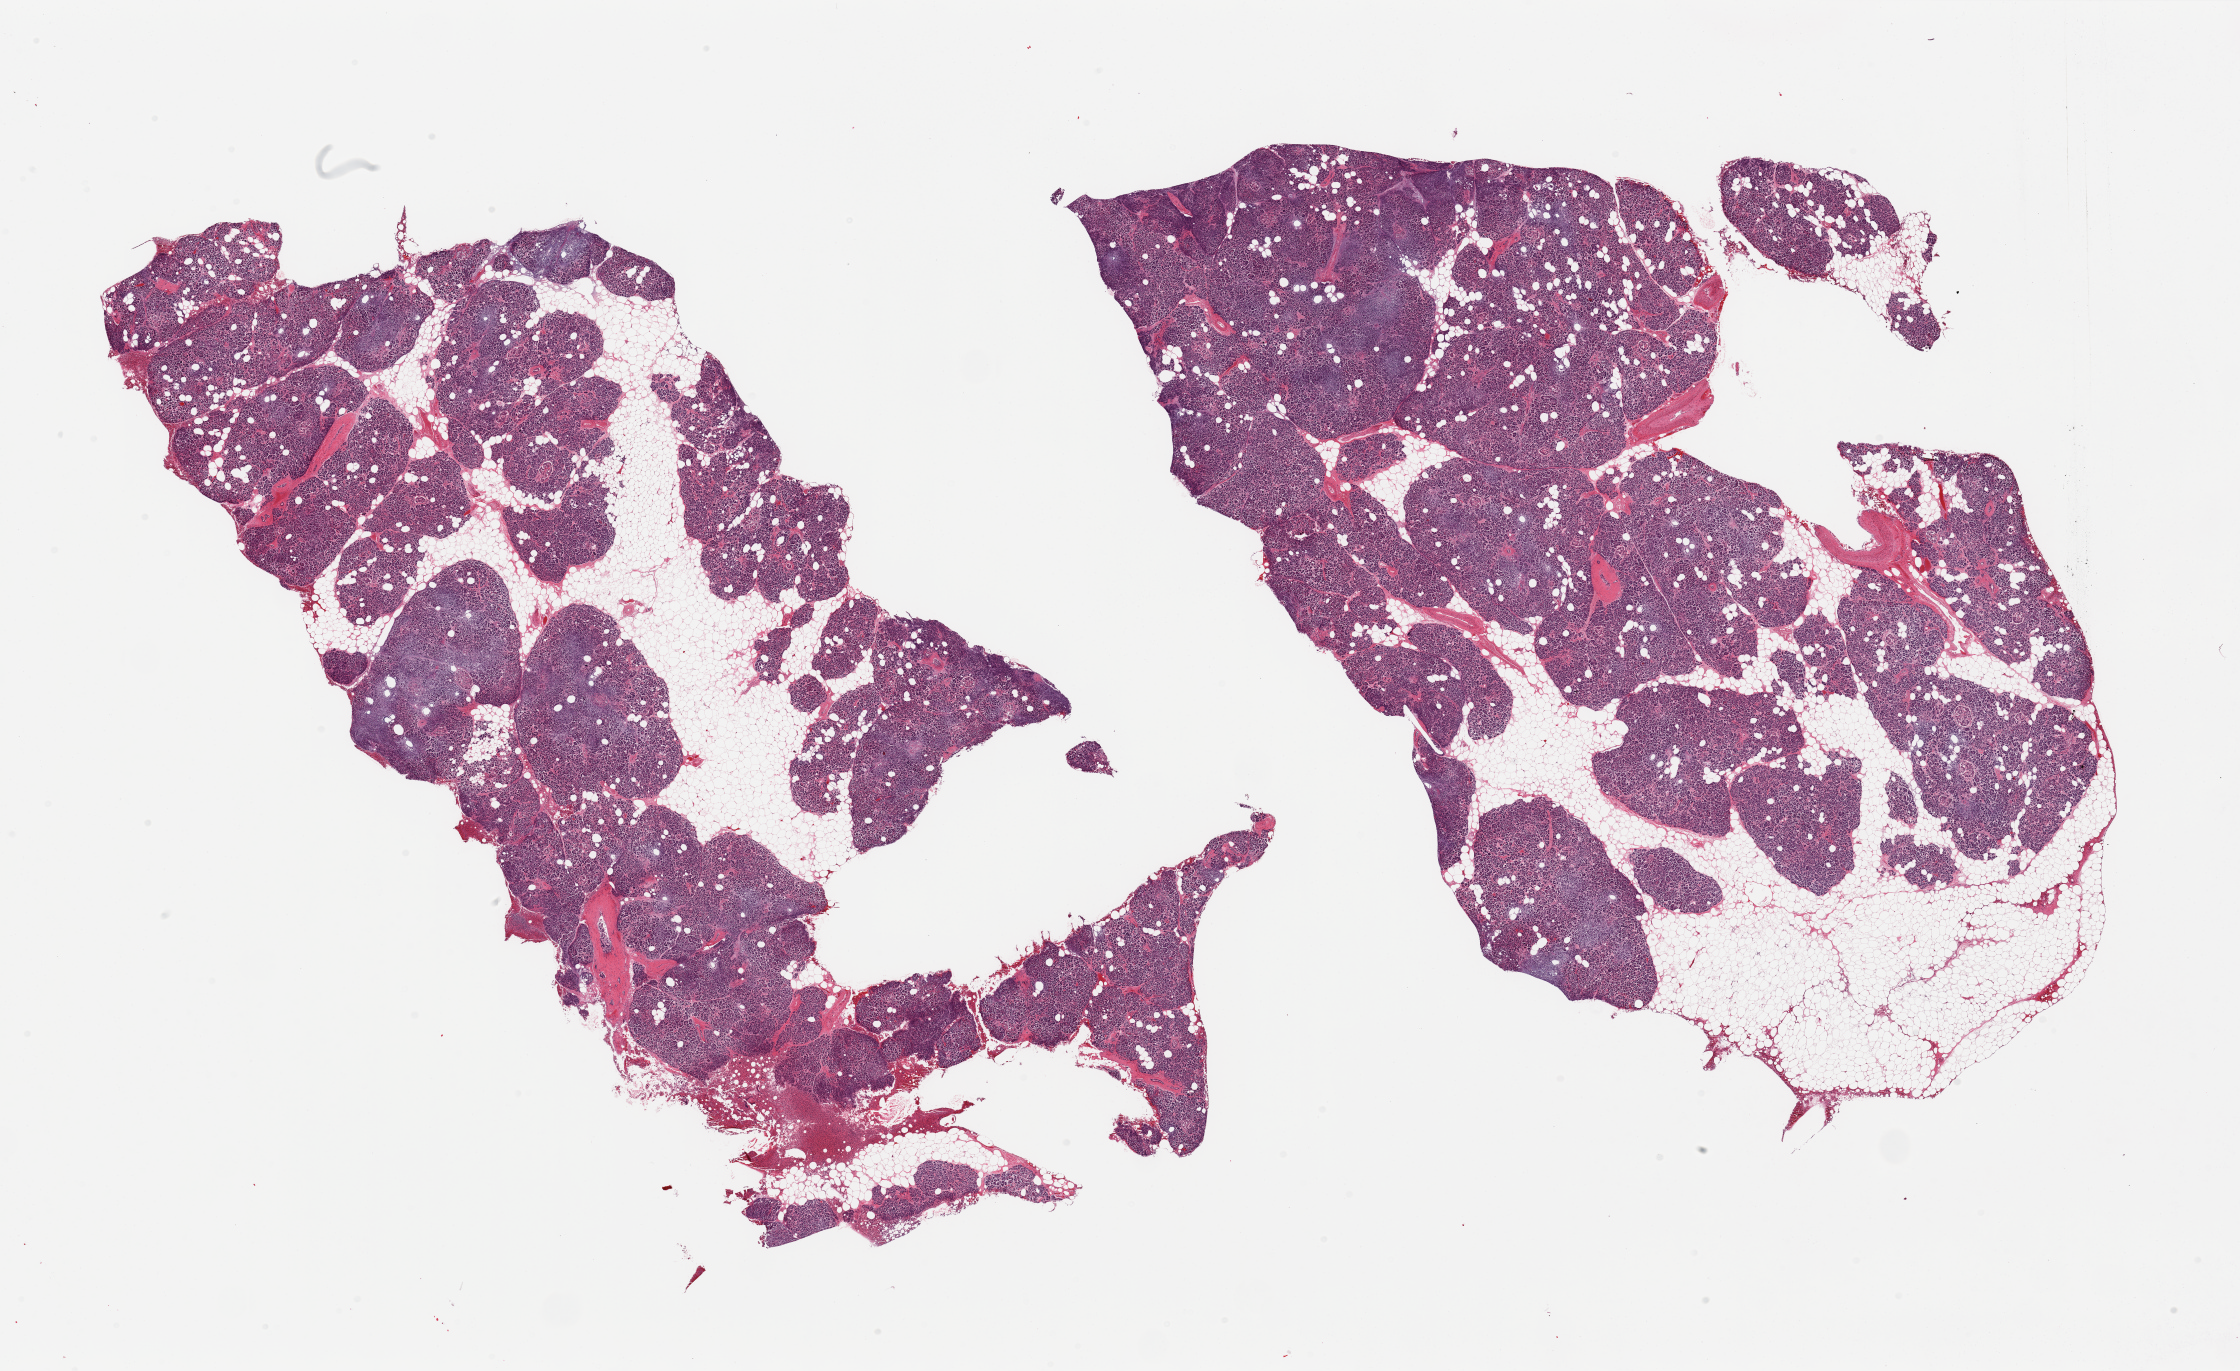
Whole-slide image, haematoxylin and eosin stain, whole scanned area (about 35.4 x 21.7 mm) shown as a low-resolution overview; PAXgene-fixed, paraffin-embedded tissue; sampled site (target tissue): pancreas; donor tissue sample. Donor: male.
* pathologist's review note for this sample: 2 pieces; ~30% is internal and attached fat, moderate to severe autolysis, mild fibrosis